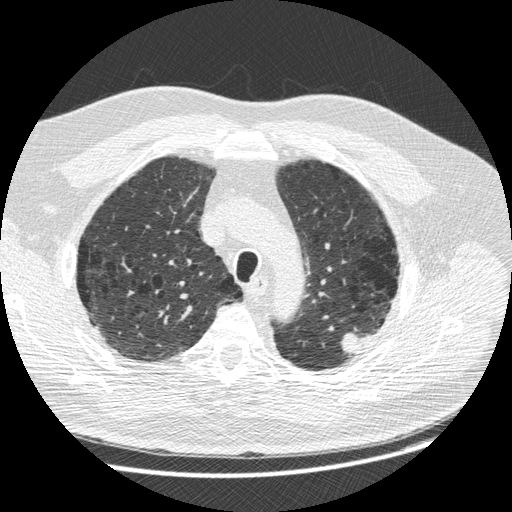
Low-dose screening chest CT, one axial slice; position 204 of 258 along the scan axis; reconstruction kernel STANDARD; 120 kVp; lung window (W 1500 / L -600 HU); 1.25 mm slice thickness; 512 × 512 image matrix, field of view 370 × 370 mm.
Annotated regions visible in this slice (expert manual segmentation):
- lesion 1 (tumor, upper lobe of left lung): box from (x=341, y=332) to (x=370, y=354) px